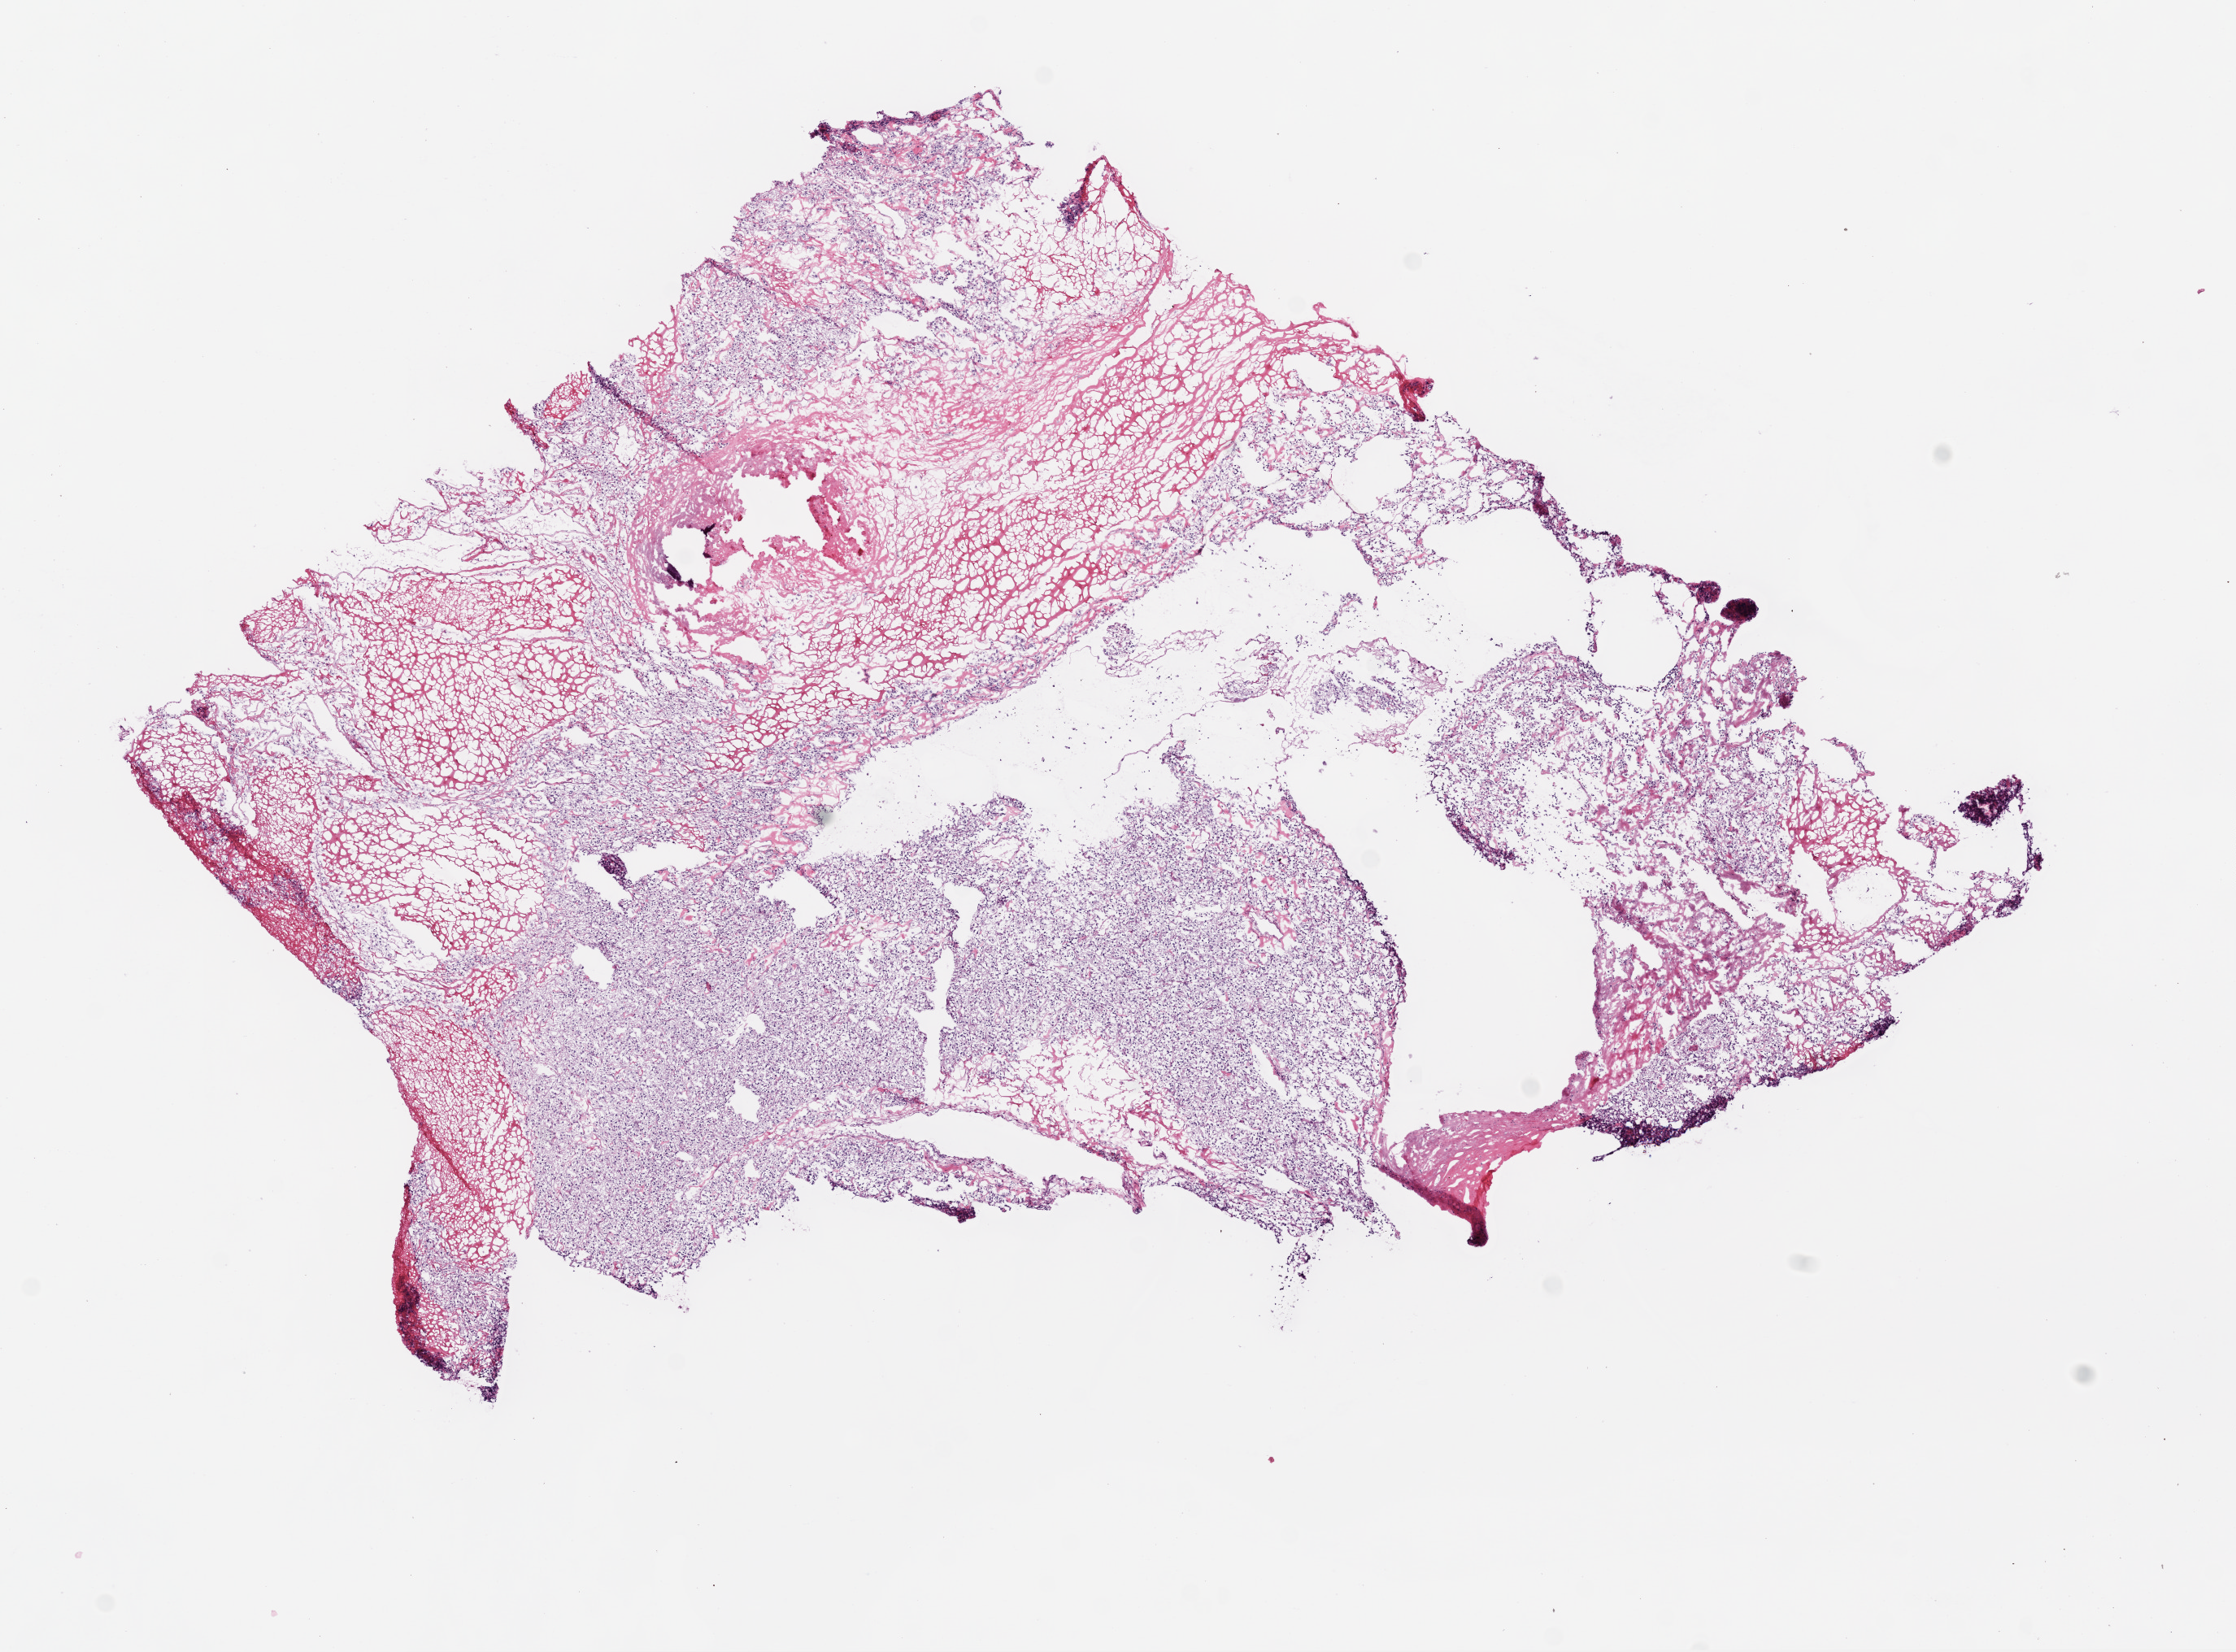
Digitized H&E tissue section (whole slide) — whole scanned area (about 11.0 x 8.2 mm, acquisition: 20x scan) shown as a low-resolution overview; frozen section from the top of the tissue portion; primary tumour sample from the kidney. Male, age 69 years at initial diagnosis. Histologic grade: G3 (poorly differentiated). Composition of this section per pathologist review: tumour cells 75%, tumour nuclei 80%, normal cells 0%, stromal cells 5%, necrosis 20%.
* AJCC pathologic stage: I
* histologic diagnosis: Clear cell adenocarcinoma, NOS